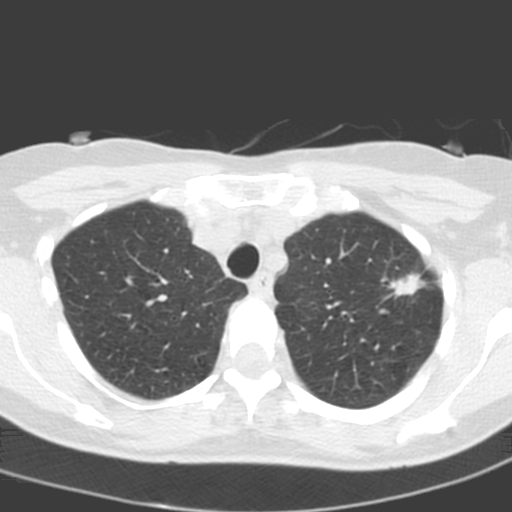
Low-dose screening chest CT, one axial slice. Slice 155 of 193 in the series (ordered by position). Lung window (W 1500 / L -600 HU). 3.2 mm slice thickness. 512 × 512 image matrix, field of view 272 × 272 mm.
Structures marked on this image (expert manual segmentation):
- lesion 1 (tumor, upper lobe of left lung): bounding box (x1, y1, x2, y2) in pixels: (389, 273, 426, 297)